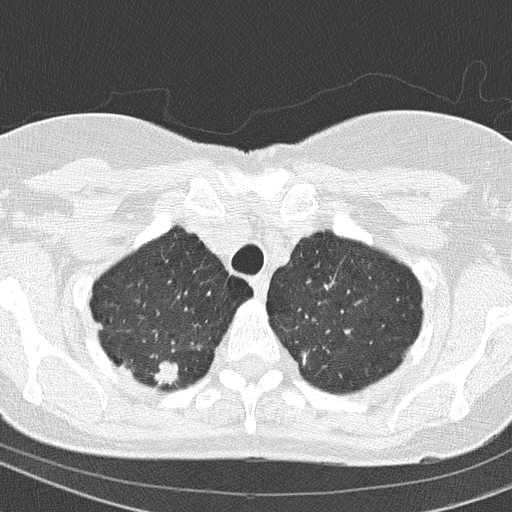
Low-dose screening chest CT, one axial slice. Position 132 of 154 along the scan axis. Reconstruction kernel B50f. Lung window (W 1500 / L -600 HU). 512 × 512 image matrix, field of view 288 × 288 mm.
Annotated regions visible in this slice (manually delineated by an expert):
- lesion 1 (tumor, upper lobe of right lung): box from (x=154, y=361) to (x=178, y=385) px